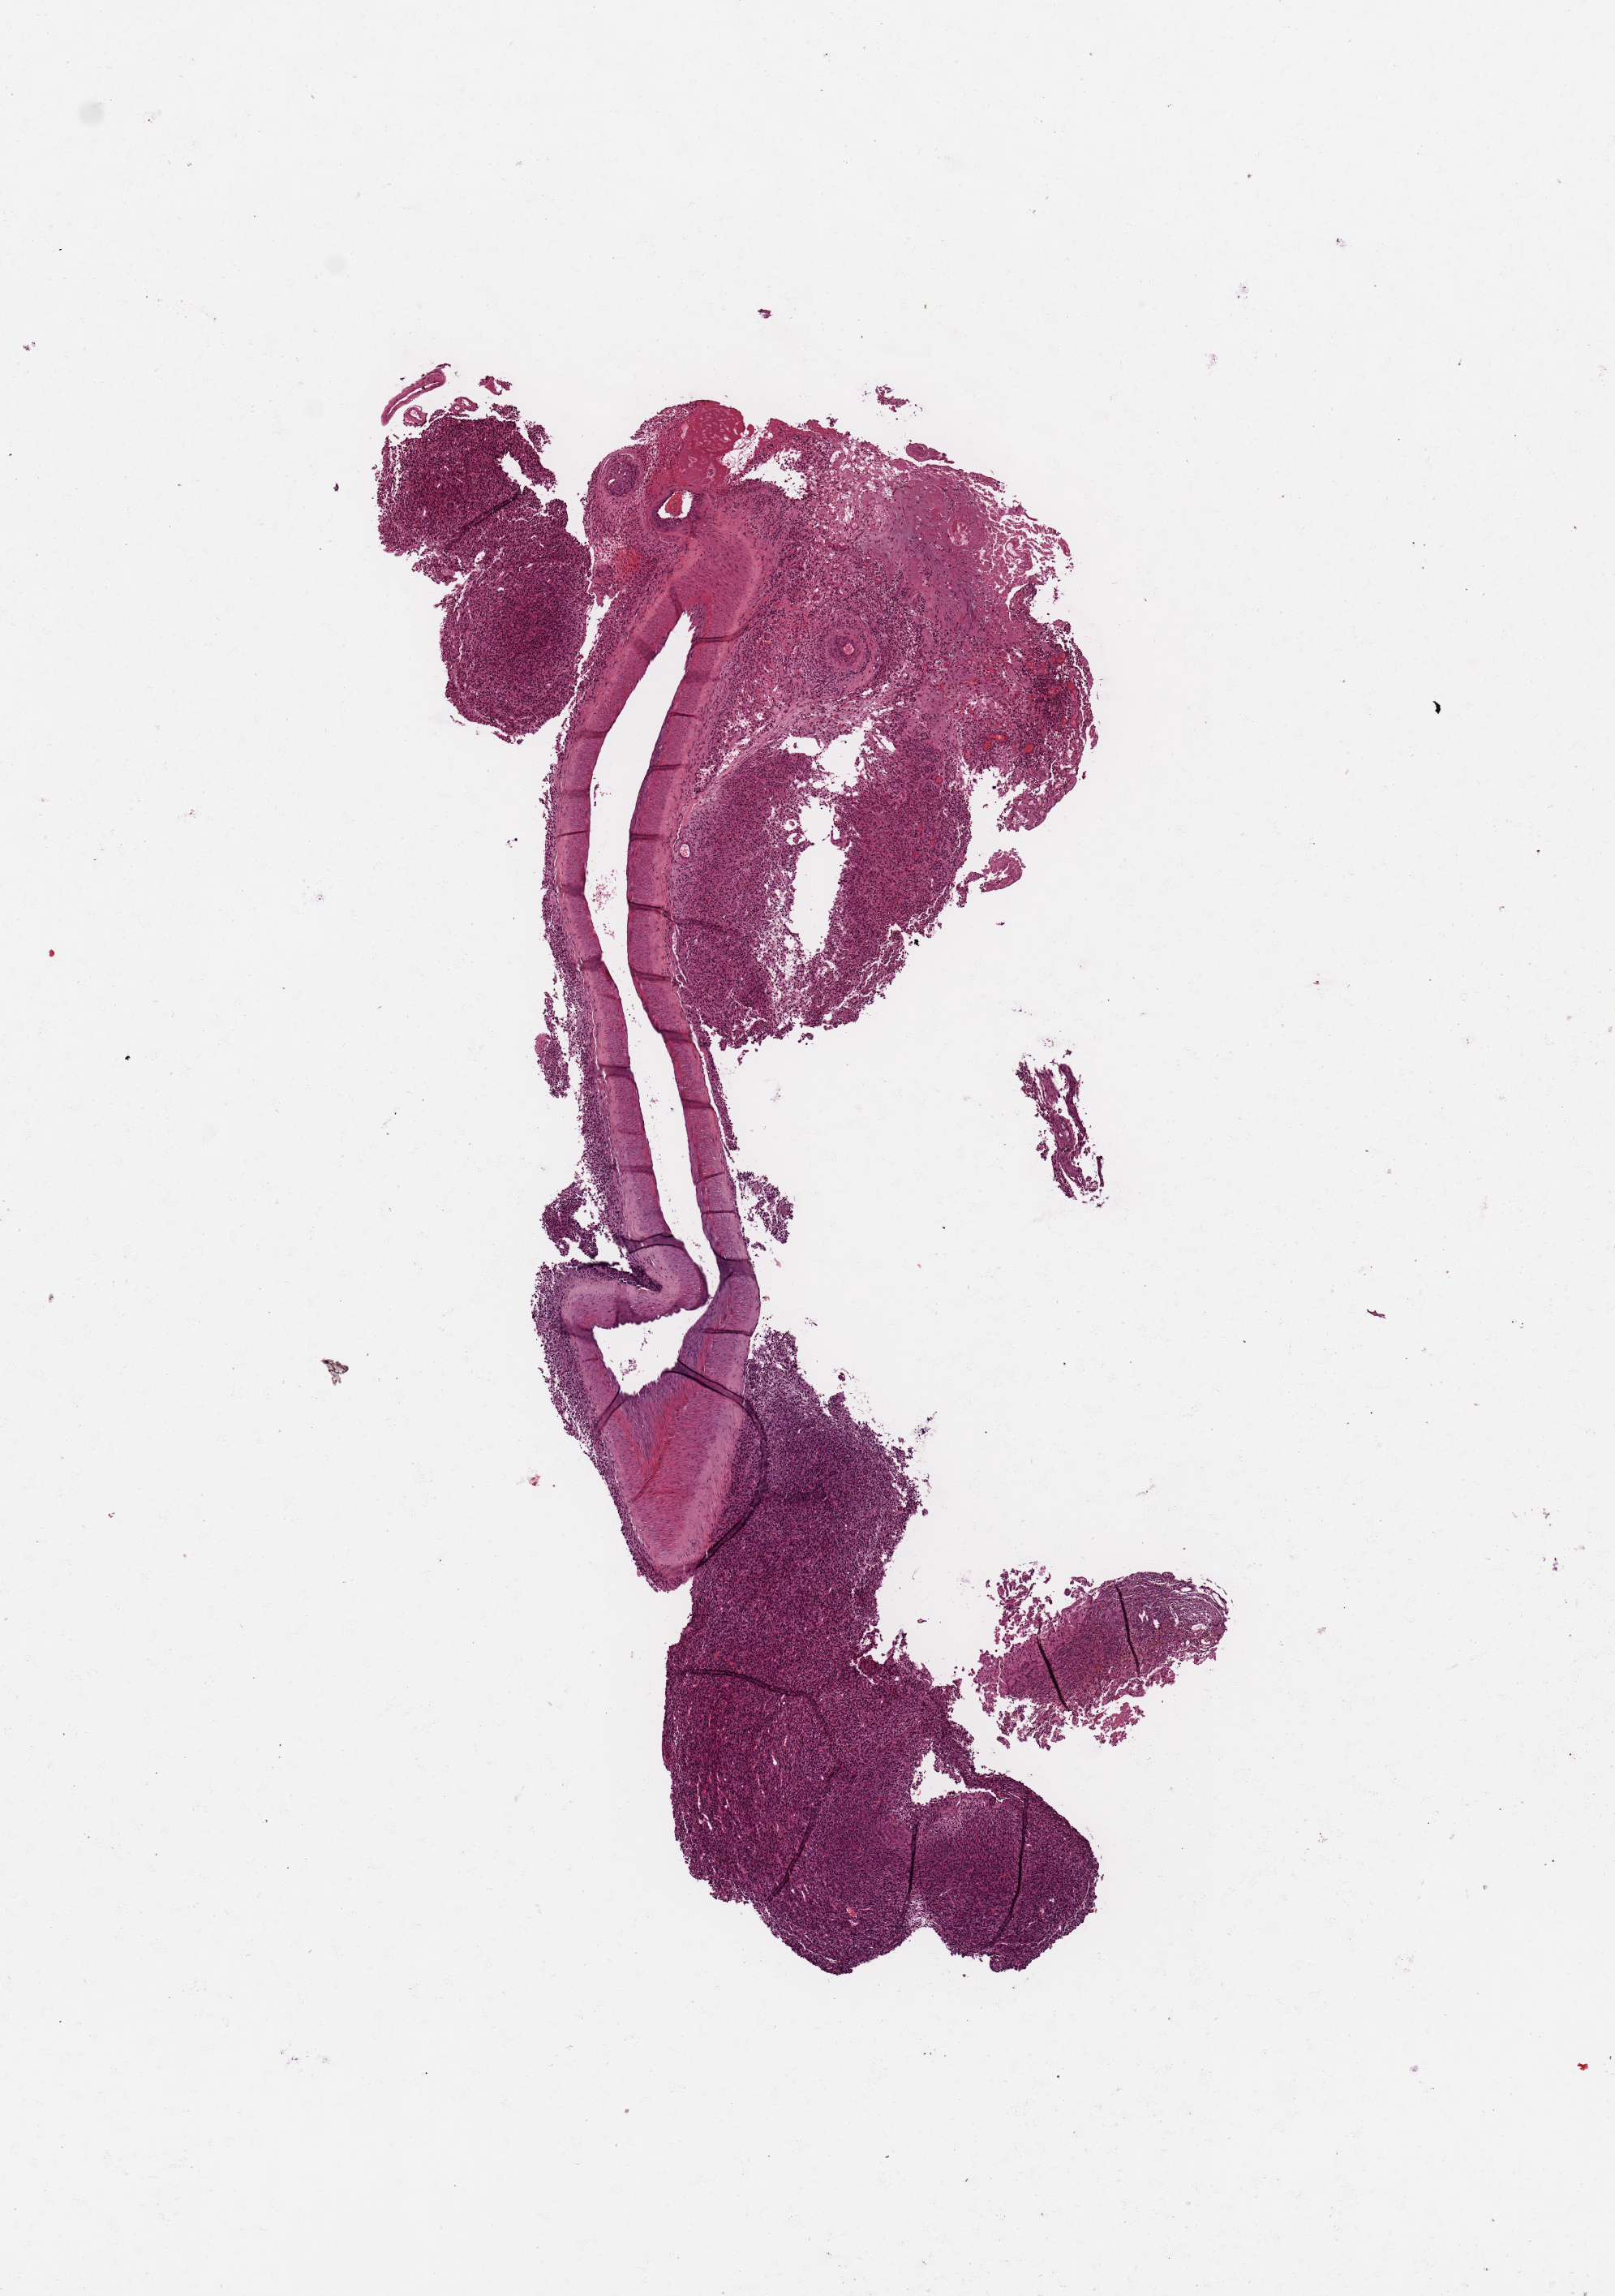
Whole-slide histology image, Hematoxylin and eosin (H&E) stained — shown as a low-resolution overview of the whole scanned area (about 7.9 x 11.2 mm), tumour tissue sample, sampled site: frontal lobe. Patient: male, age 49 years.
Diagnosis: Glioblastoma.